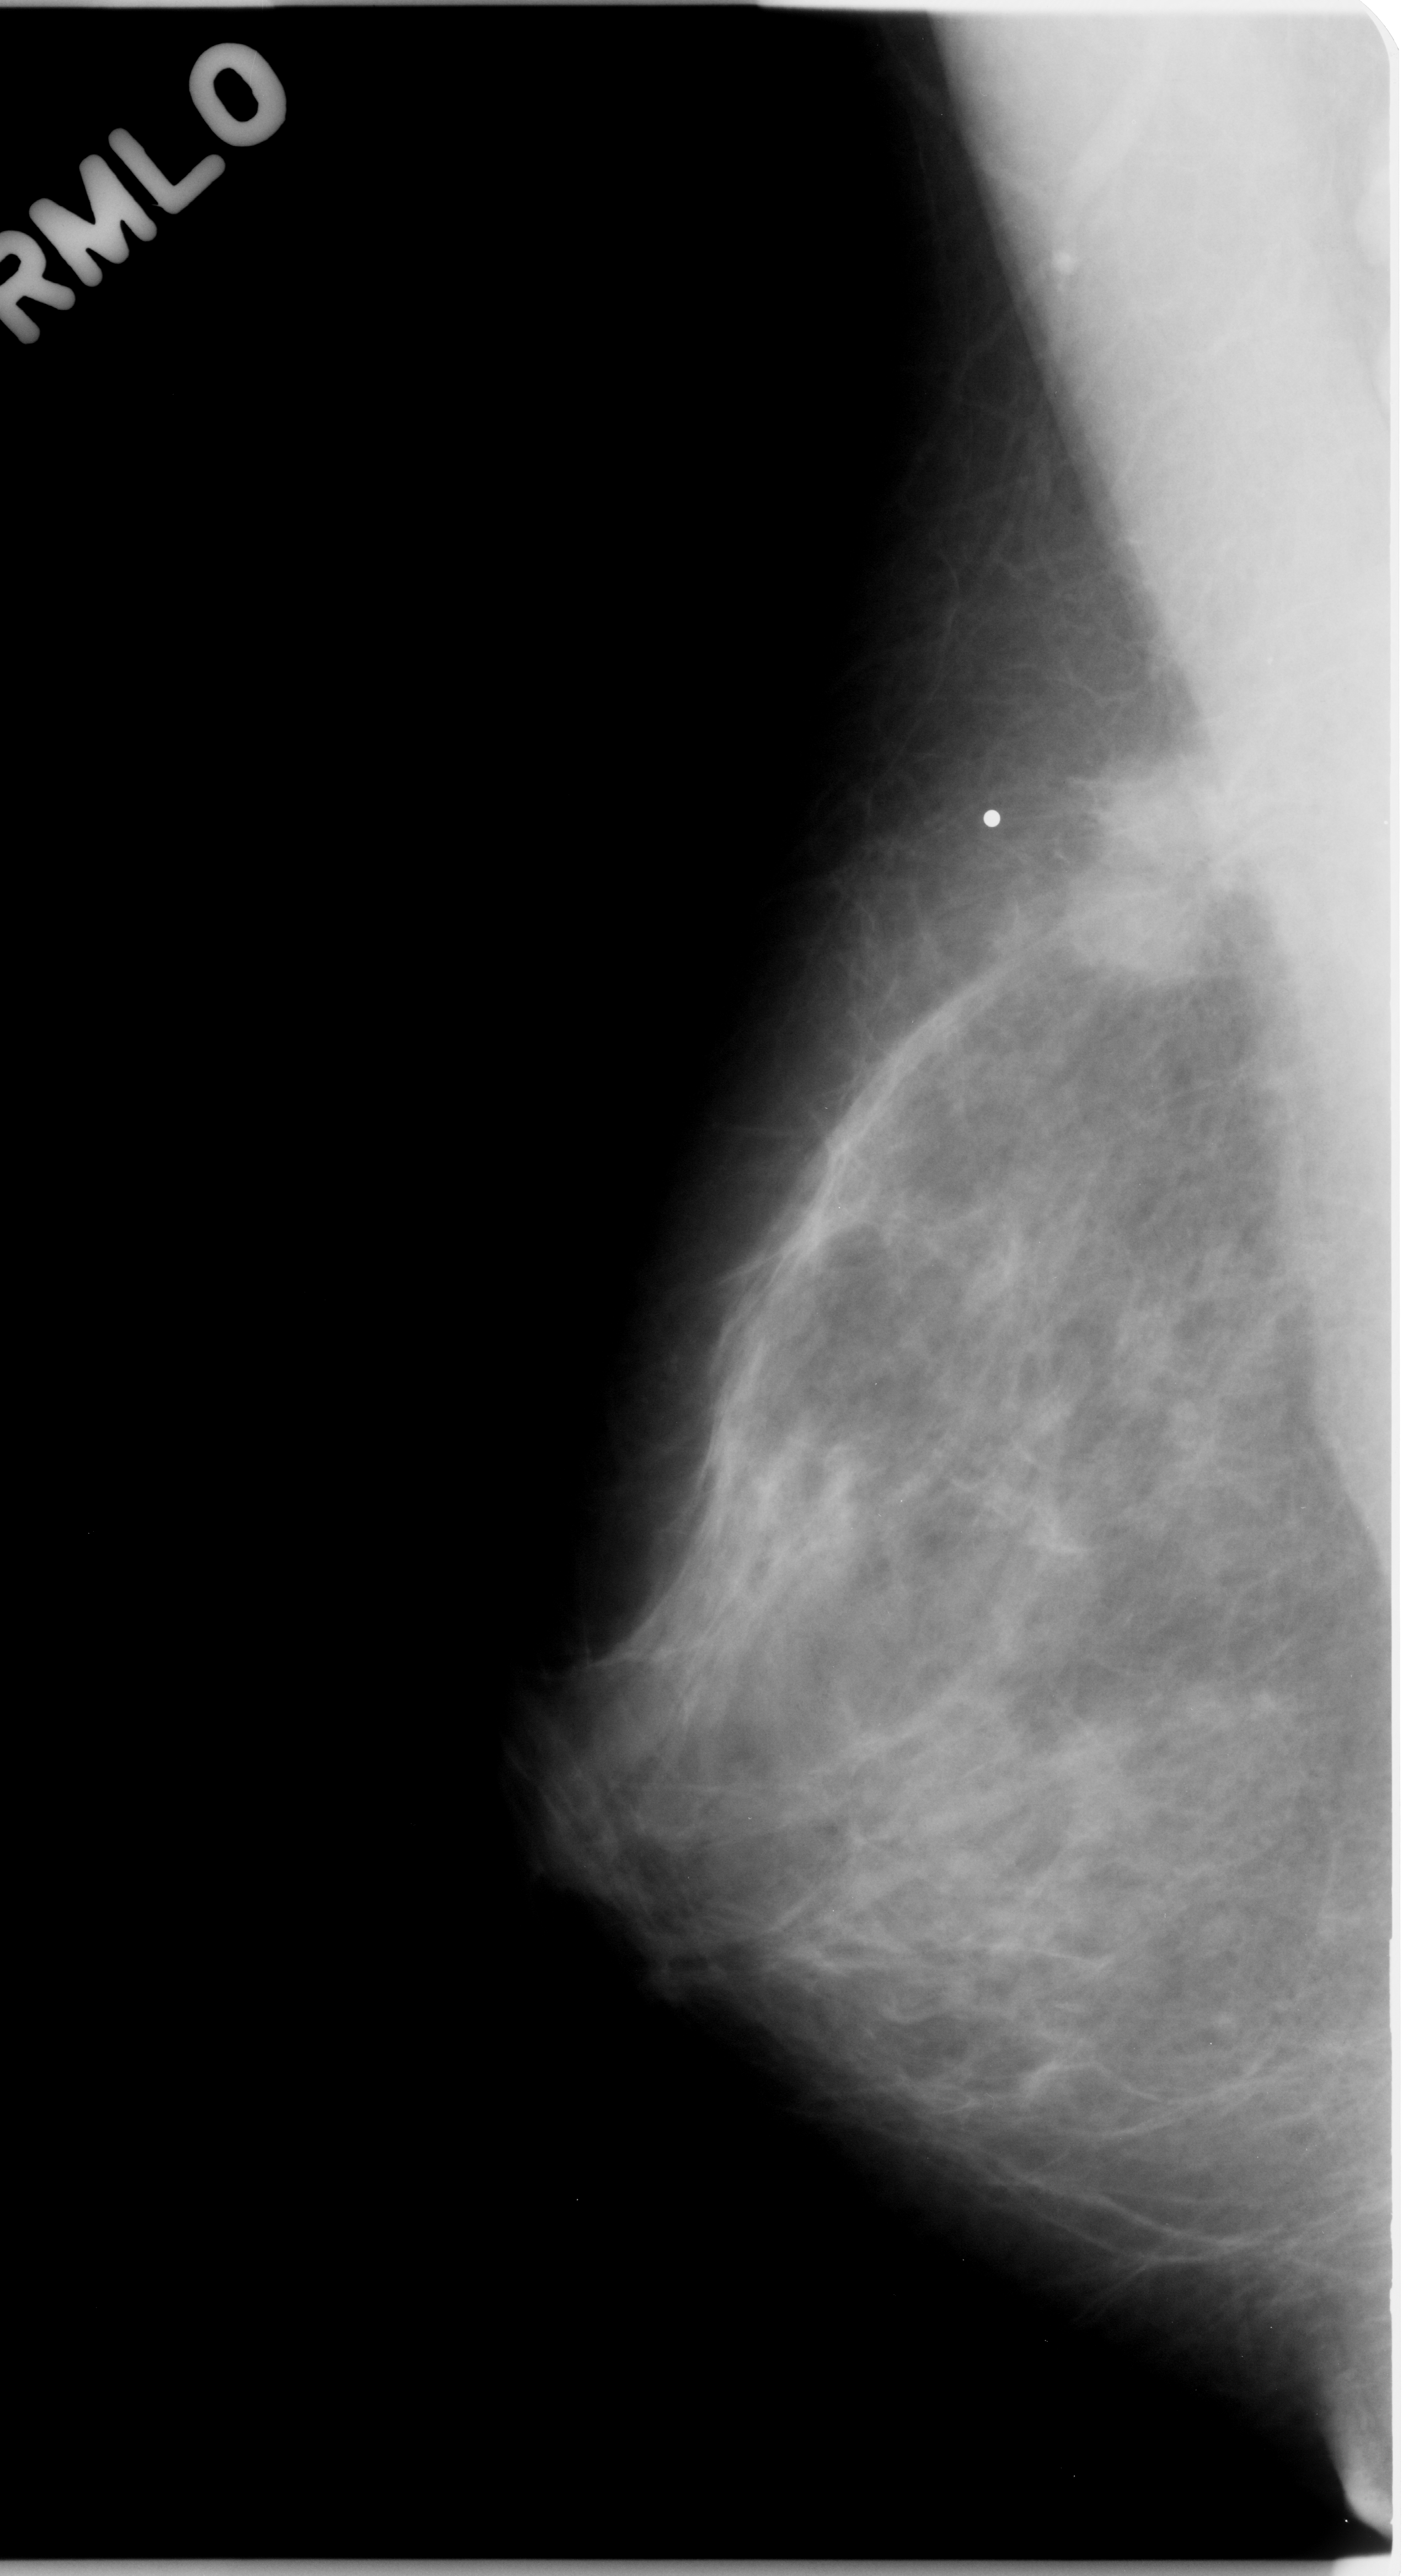
Mammogram (digitized film), right breast, mediolateral oblique (MLO) view.
Marked abnormality: mass, shape irregular, margins spiculated; BI-RADS assessment category 5; subtlety rating 5 on a 1 (subtle) to 5 (obvious) scale; pathology result (as recorded, not read from the image): malignant.